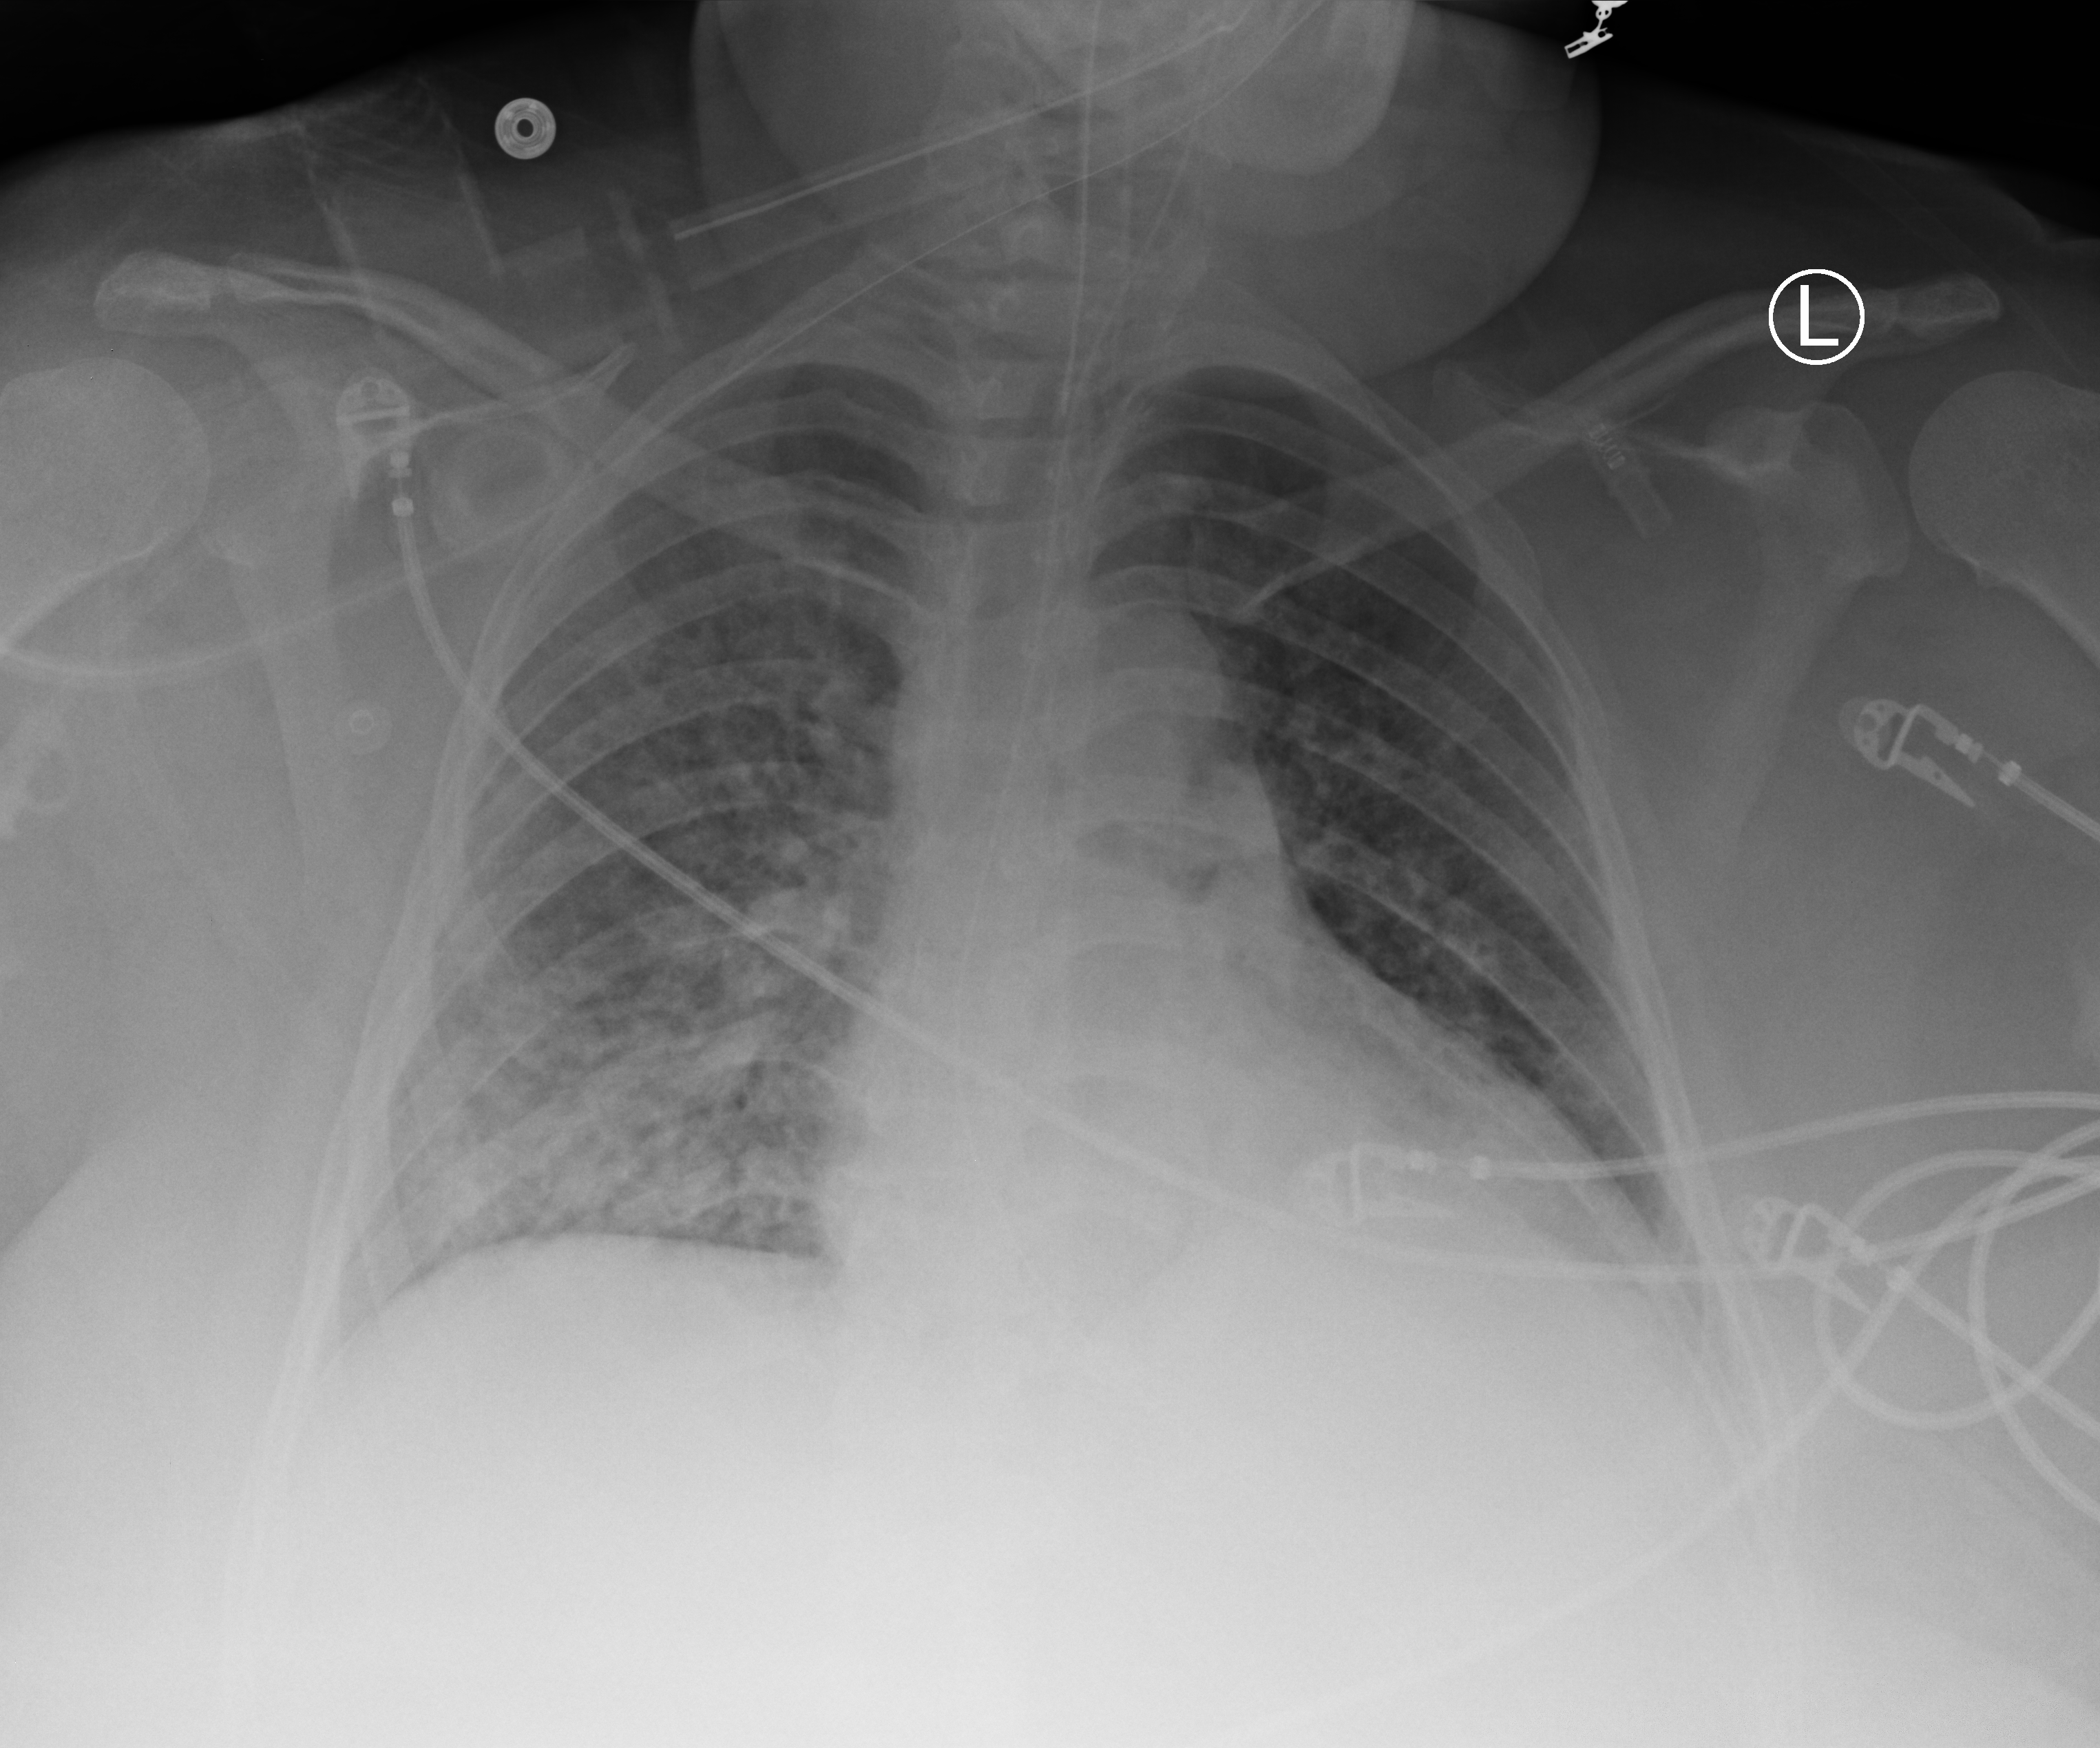
Bedside chest radiograph (computed radiography); anteroposterior (AP) projection. Female patient hospitalised with COVID-19, age 18–59 years.
Hospital-stay facts (about this admission, not read from this image; timing relative to this image not recorded): admitted to intensive care during this hospital stay: yes; COPD (admission record): no.